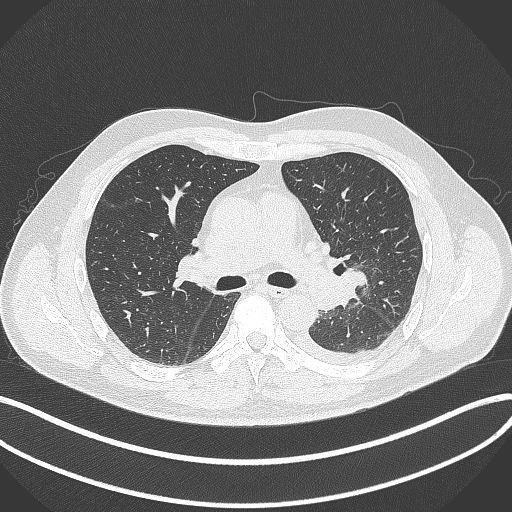
Chest CT, one axial slice. Slice 219 of 342 in the series (ordered by position). Reconstruction kernel B70f. 120 kVp. Lung window (W 1500 / L -600 HU). 1 mm slice thickness. 512 × 512 image matrix. Patient: male, 58 years. From the clinical record (not read from this slice): clinical TNM (as recorded): T3 N1 M1b; histopathological grade: G3.
Structures marked on this image (bounding box drawn by a radiologist):
- lung tumour (recorded histology: small cell carcinoma): bounding box <340,264,369,294> (left, top, right, bottom; pixels)